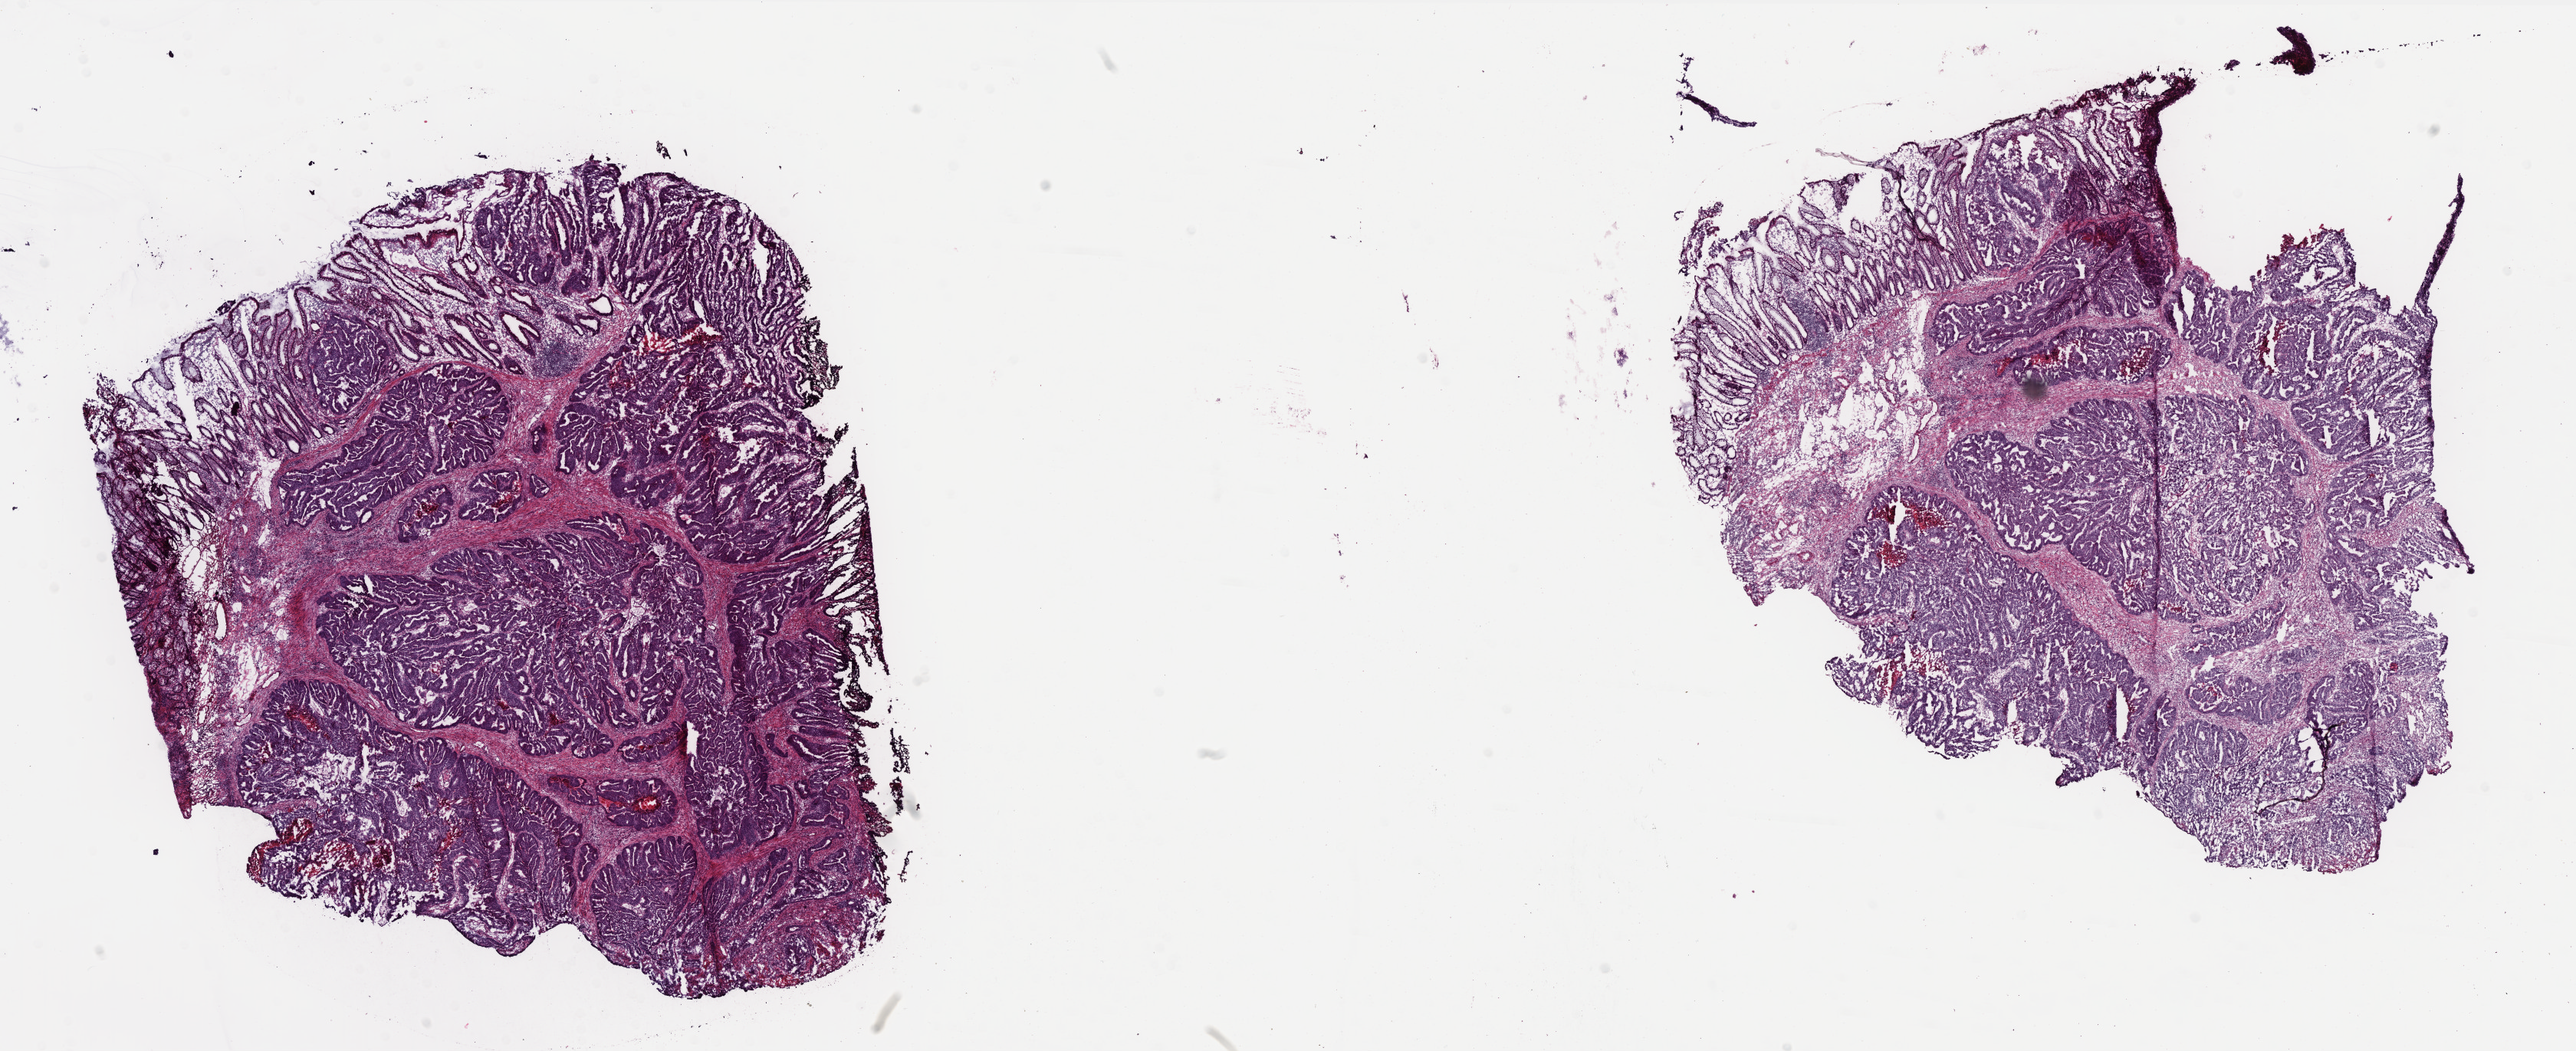
H&E-stained whole-slide image, whole scanned area (about 26.9 x 11.0 mm, slide scanned at 40x) shown as a low-resolution overview; frozen section from the bottom of the tissue portion; colon, primary tumour sample. Female patient; age at initial diagnosis 70 years. Pathologist review of this section (percent, as recorded): tumour cells 65%, tumour nuclei 75%, normal cells 20%, stromal cells 10%, necrosis 5%. Infiltration values recorded for this section: lymphocyte infiltration 5%, monocyte infiltration 1%, neutrophil infiltration 1%.
AJCC pathologic stage: IV. Diagnosis: Adenocarcinoma, NOS. Lymph nodes positive (case pathology): 0 of 13 examined.